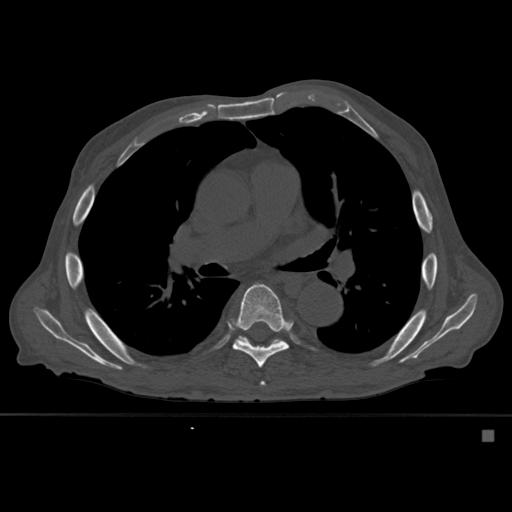
CT including the spine, one axial slice; position 367 of 527 along the scan axis; bone window (W 1800 / L 400 HU); 512 × 512 image matrix, field of view 373 × 373 mm. Patient: male, 78 years. From the clinical record (not read from this slice): primary cancer: prostate.
Outlined on this slice (semi-automatic segmentation, software-assisted and operator-edited):
- T6 vertebra: bounding box [x1, y1, x2, y2] px = [261, 382, 265, 386]
- T7 vertebra: [218, 283, 289, 368]
- T8 vertebra: [240, 337, 282, 342]